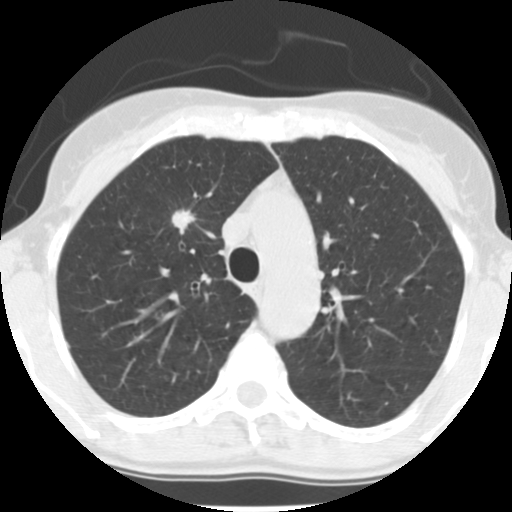
Axial slice from a low-dose chest CT screening exam. Second annual screen. Lung window (W 1500 / L -600 HU). 140 kVp. Female, age 56 years at enrolment. Former smoker at enrolment.
Expert-annotated lung lesion, bounding box <159,200,202,244> (left, top, right, bottom; pixels). Reader record for this screening exam (exam-level; its link to the box is not recorded): non-calcified nodule or mass ≥4 mm, right upper lobe, 12 × 9 mm, spiculated (stellate) margins, soft tissue attenuation, pre-existing on the prior screen: yes; interval growth: no. Official screen result: positive, other. Later outcome: lung cancer diagnosed 350 days after this screen — adenocarcinoma, NOS, right upper lobe, moderately differentiated (G2), stage IA (AJCC 6th edition), 19 mm at pathology.